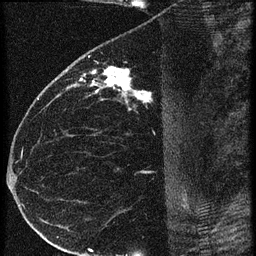
Breast MRI (dynamic contrast-enhanced), one sagittal slice. 3 images stored at this slice position (order not interpretable as contrast timing). 1.5 T. TE 4.2 ms, TR 20.4 ms. 256 × 256 image matrix. Female patient, age 35 years. From the clinical record (not read from this slice): setting: breast cancer imaged before/during neoadjuvant chemotherapy; receptor status: HR-positive, HER2-negative.
Annotated regions visible in this slice (semi-automatically segmented with operator editing):
- analysis volume of interest (the breast-tissue region the enhancement analysis was run in; not a lesion): bounding box <65,60,169,119> (left, top, right, bottom; pixels)
- tumour enhancement mask (voxels above the 90 % enhancement threshold inside the analysis volume of interest): <71,68,152,101>